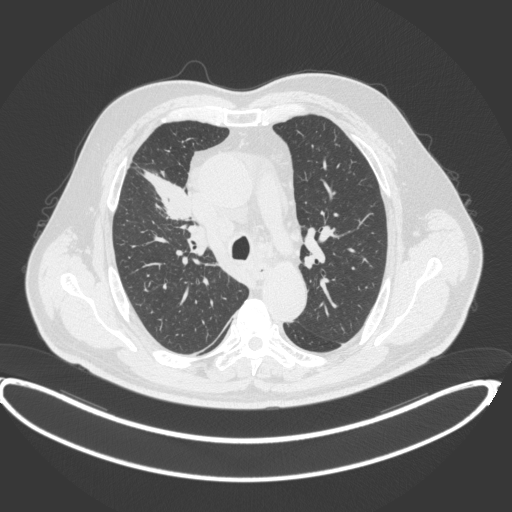
Chest CT, one axial slice. Slice 281 of 395 in the series (ordered by position). 120 kVp. Lung window (W 1500 / L -600 HU). 1 mm slice thickness. 512 × 512 image matrix, field of view 448 × 448 mm. Patient: male, 62 years. From the clinical record (not read from this slice): clinical TNM (as recorded): T1c N3 M1c.
Annotated regions visible in this slice (bounding box drawn by a radiologist):
- lung tumour (recorded histology: adenocarcinoma): box from (x=139, y=166) to (x=194, y=223) px